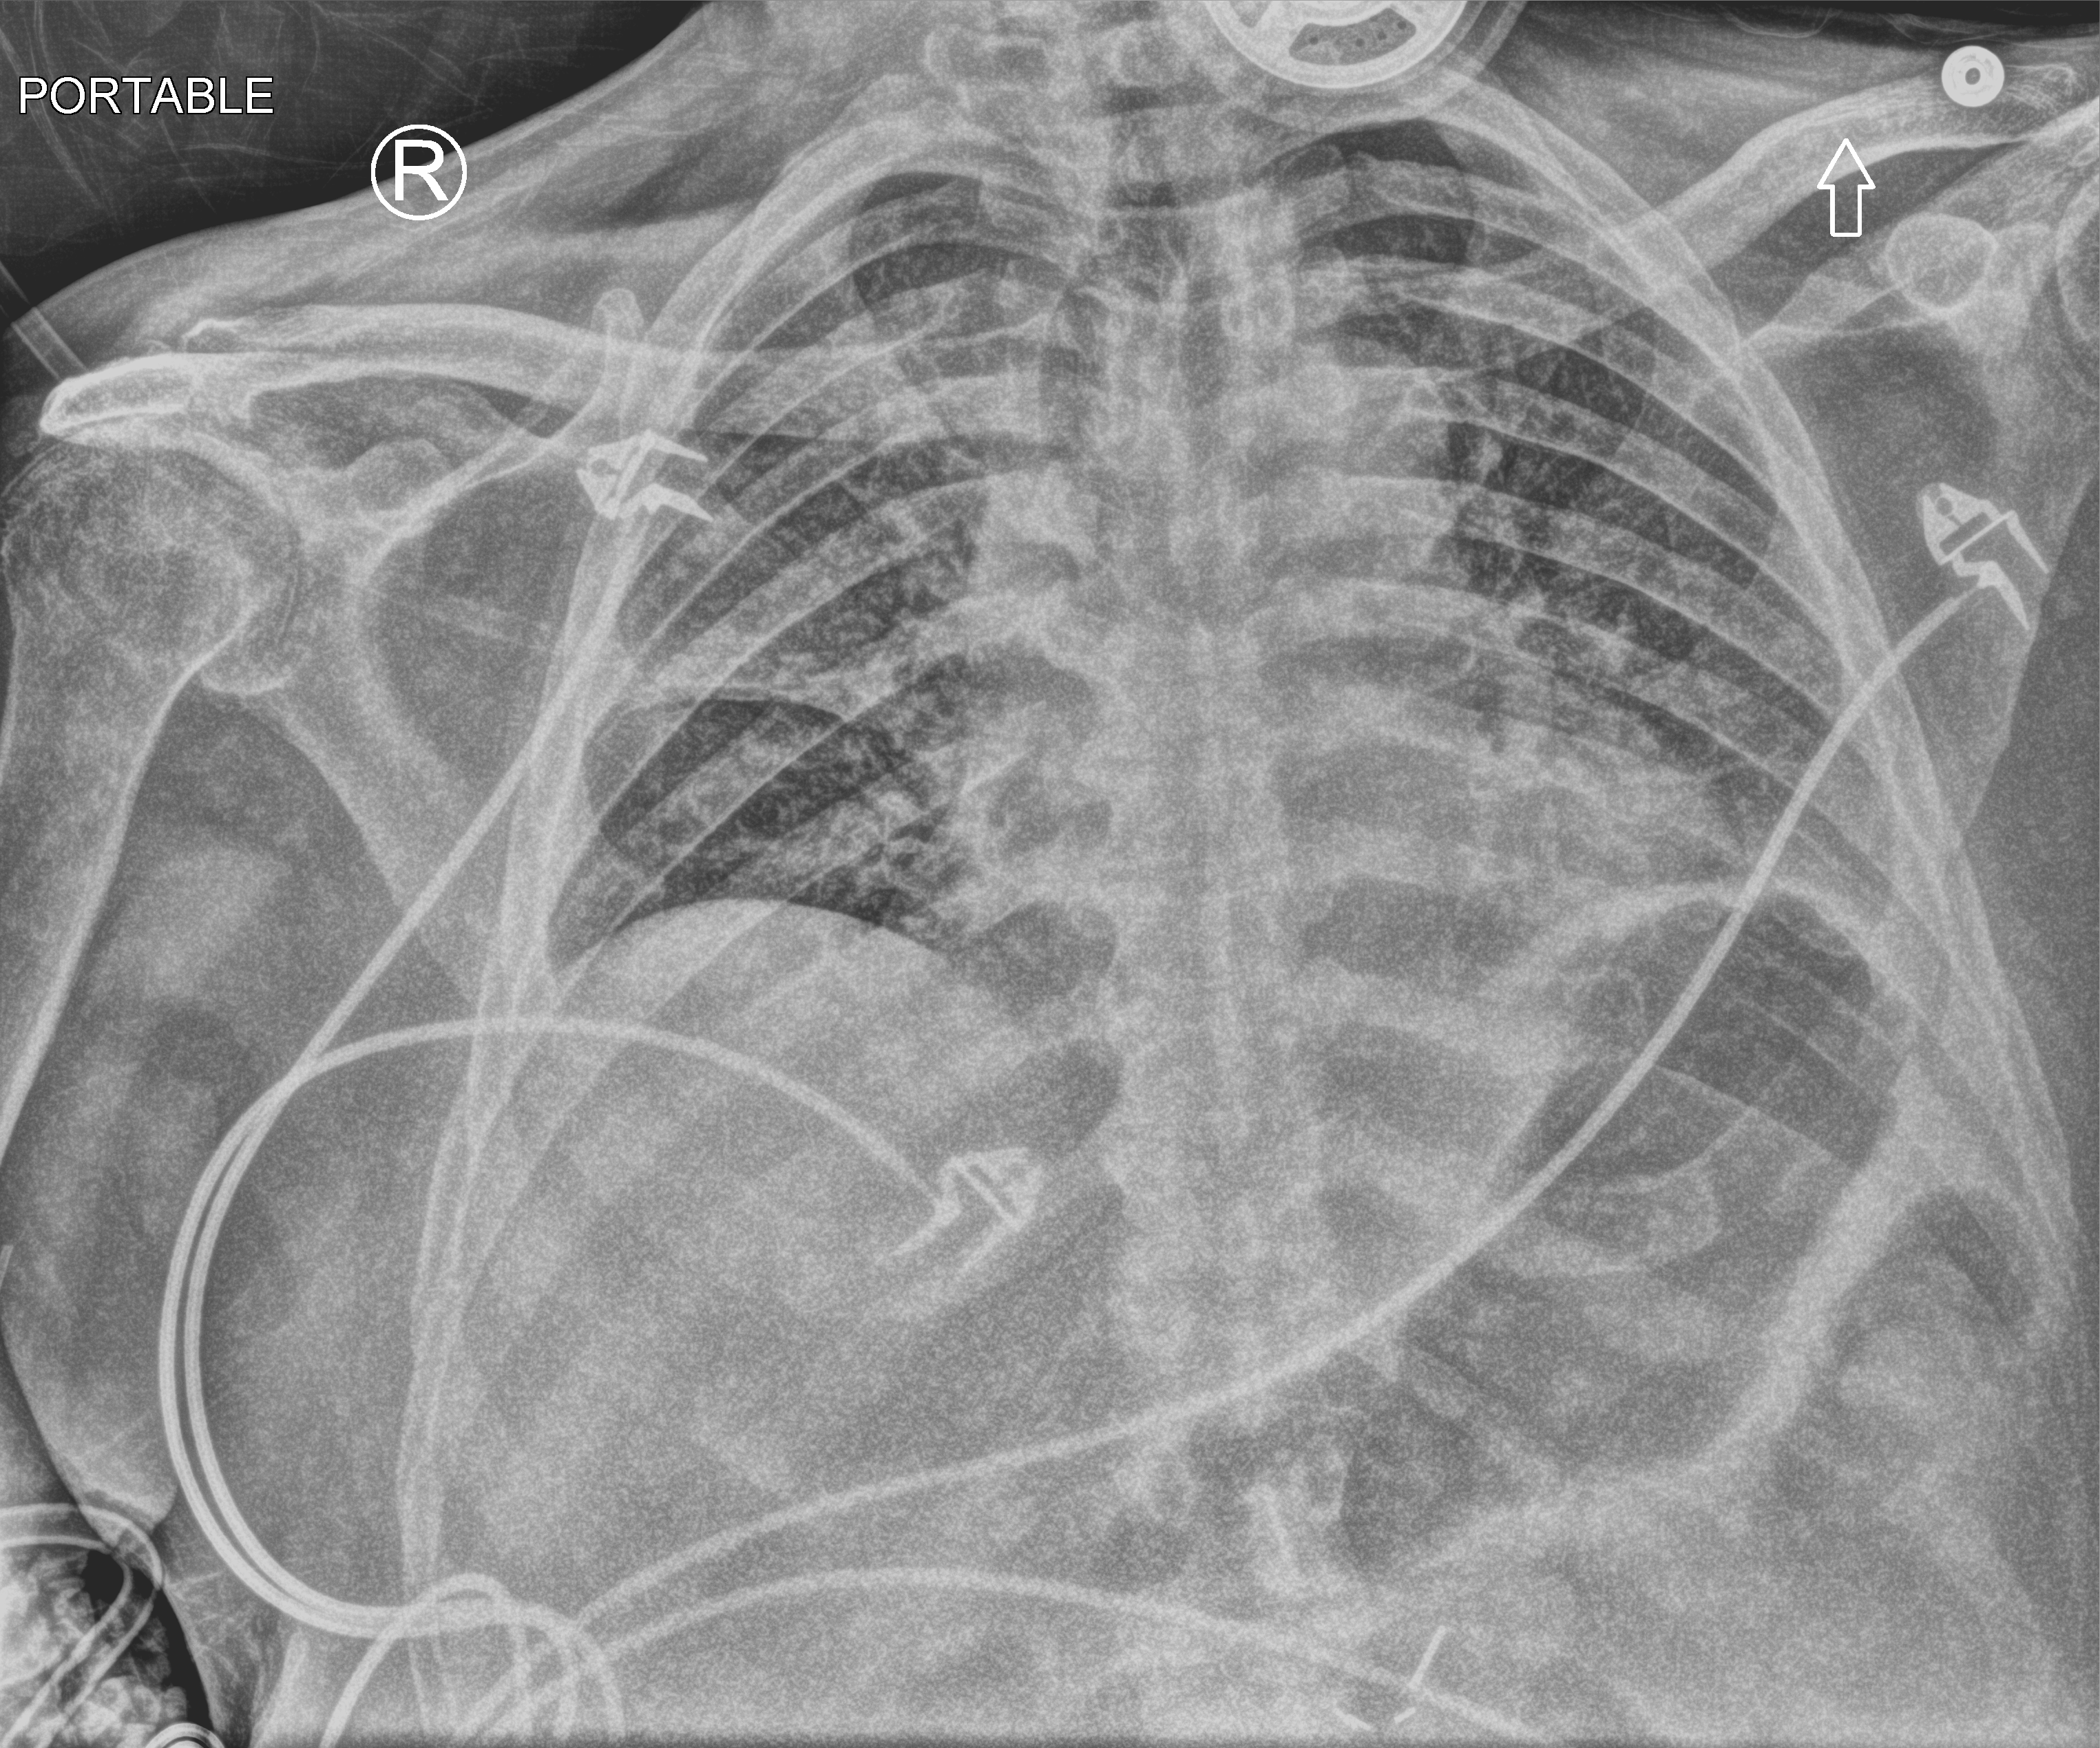
Chest X-ray (portable); anteroposterior (AP) projection. Patient hospitalised with COVID-19; male, aged 75–90 years.
Hospital-stay facts (about this admission, not read from this image; timing relative to this image not recorded): length of hospital stay: 12 days.